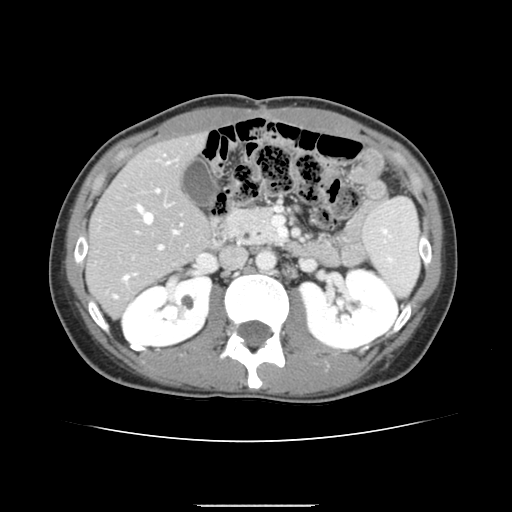
Contrast-enhanced abdominal CT, one axial slice; position 74 of 150 along the scan axis; 120 kVp; intravenous contrast given; soft-tissue window (W 400 / L 40 HU); 512 × 512 image matrix, field of view 324 × 324 mm. Female patient, age 32 years. Case-level facts recorded for this patient, not image findings: diagnosis: colorectal cancer liver metastases, imaged before liver resection; multiple liver metastases: yes; largest metastasis: 0.7 cm; disease in both lobes: no.
Outlined on this slice (manually delineated by an expert):
- hepatic veins: bounding box (x1, y1, x2, y2) in pixels: (124, 206, 177, 279)
- liver: (87, 135, 209, 316)
- planned liver remnant (the part of the liver to remain after resection): (88, 135, 210, 282)
- portal vein (with intrahepatic branches): (114, 162, 182, 298)